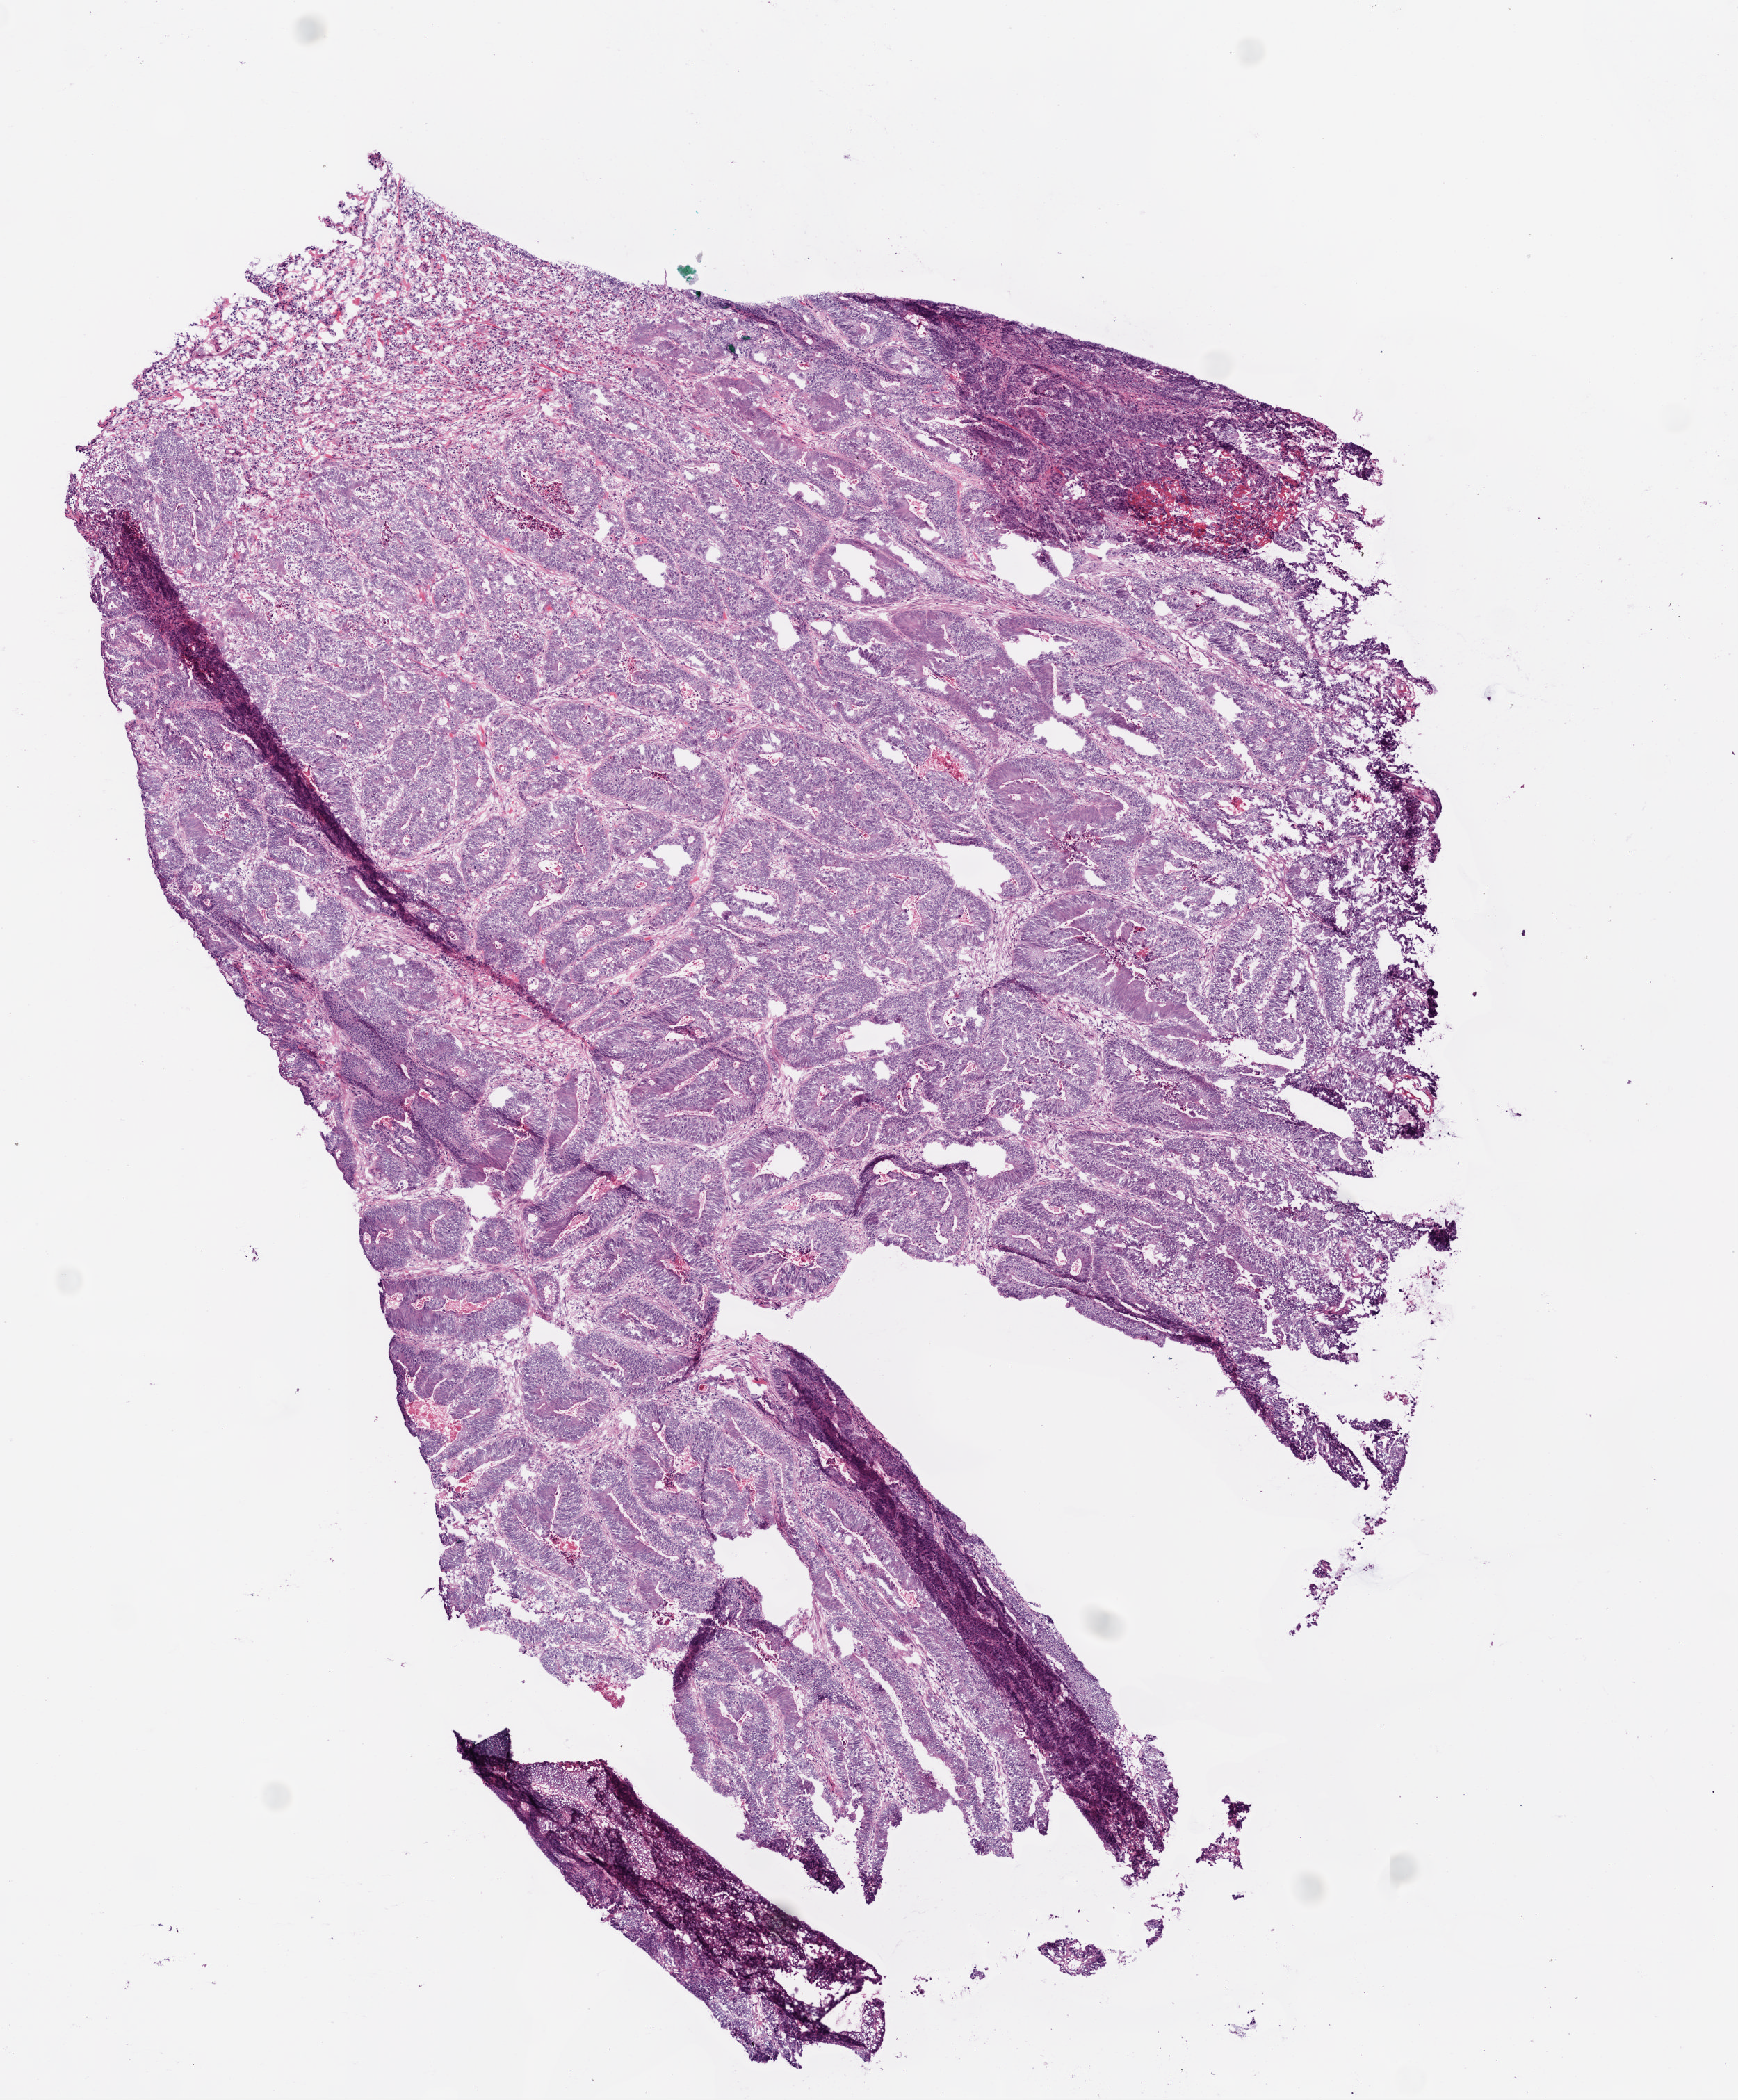
Digitized H&E tissue section (whole slide) — low-resolution overview of the scanned area, about 5.0 x 6.1 mm (acquisition: 20x scan). Frozen section from the bottom of the tissue portion. Colon, primary tumour sample. Male patient; age at initial diagnosis 85 years. Pathologist review of this section (percent, as recorded): tumour cells 80%, tumour nuclei 90%, normal cells 0%, stromal cells 20%, necrosis 0%.
AJCC pathologic stage: II (5th edition). Lymph nodes positive (case pathology): 0 of 28 examined. Histologic diagnosis: Adenocarcinoma, NOS (sigmoid colon).